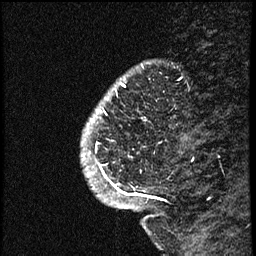
Breast MRI (dynamic contrast-enhanced), one sagittal slice; position 10 of 66 along the scan axis; dynamic contrast-enhanced study with each time point stored as its own series, time point 2 of 3 at this slice position (early post-contrast, ordered by acquisition time); 1.5 T; TE 4.2 ms, TR 17.6 ms; 256 × 256 image matrix, field of view 200 × 200 mm. Female patient. Case-level facts recorded for this patient, not image findings: setting: breast cancer imaged before/during neoadjuvant chemotherapy; receptor status: HER2-positive.
Annotated regions visible in this slice (semi-automatically segmented with operator editing):
- analysis volume of interest (the breast-tissue region the enhancement analysis was run in; not a lesion): bounding box (x1, y1, x2, y2) in pixels: (83, 69, 175, 209)
- tumour enhancement mask (voxels above the 100 % enhancement threshold inside the analysis volume of interest): (88, 82, 163, 200)